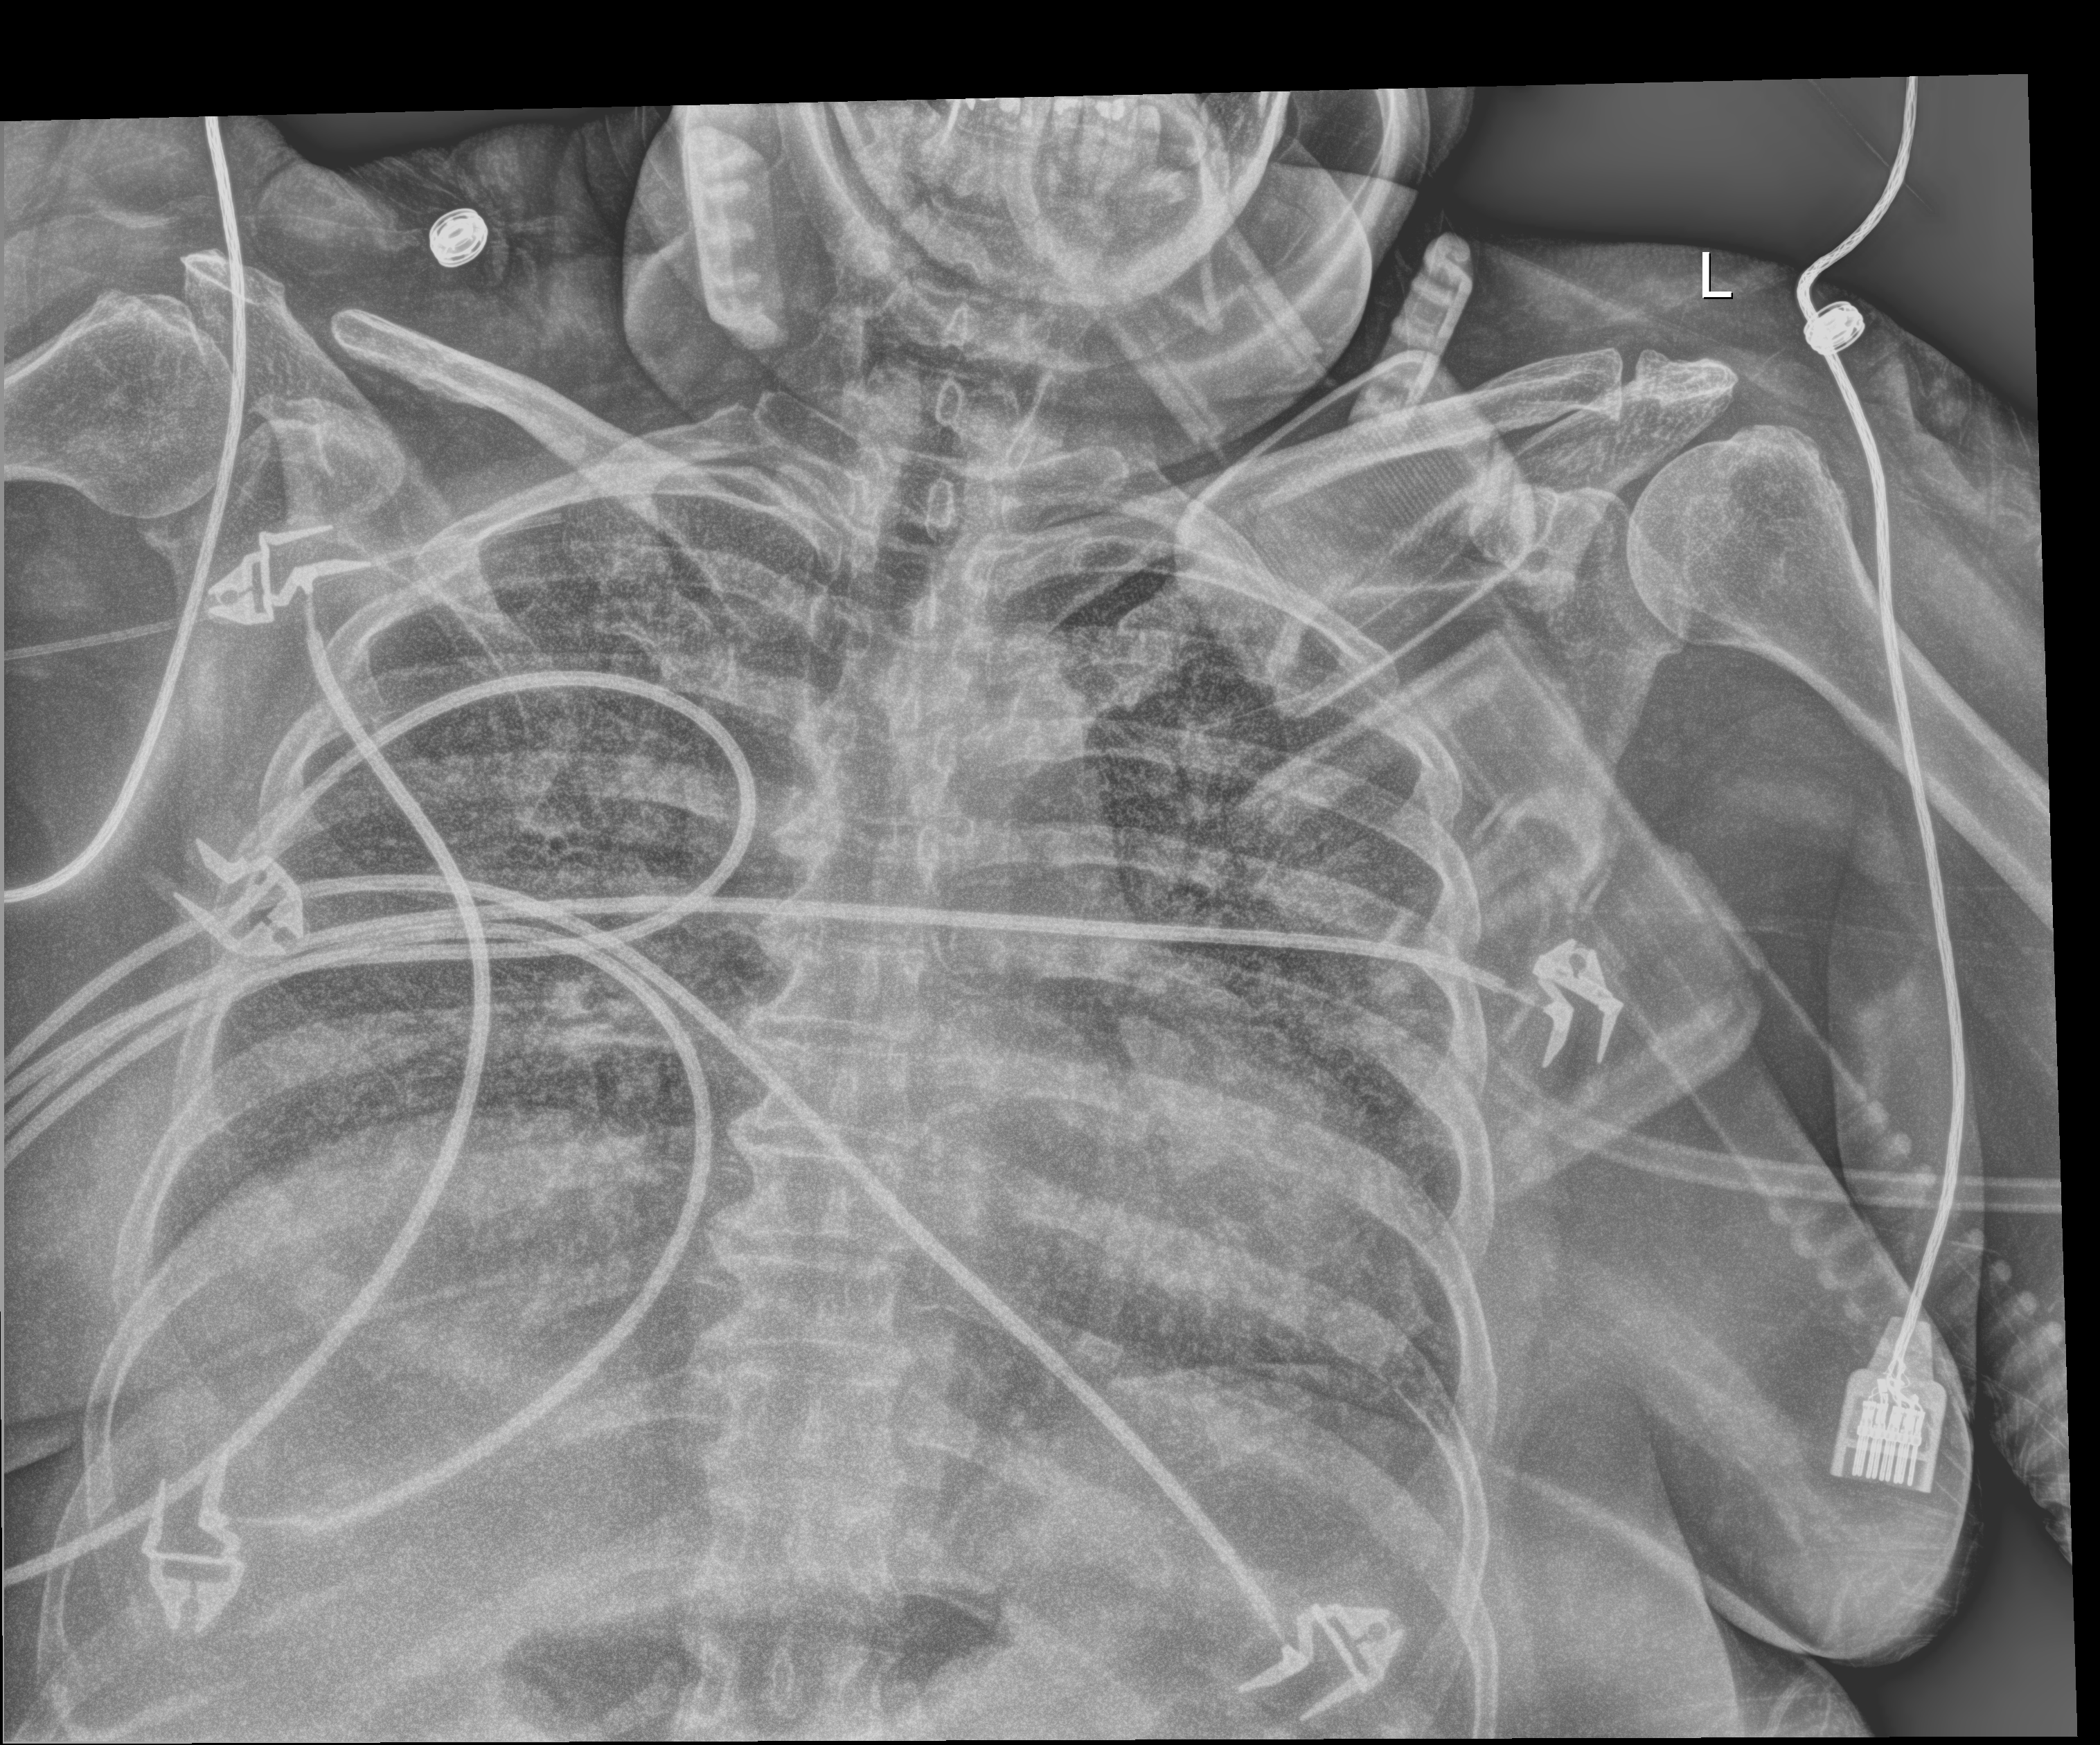
Portable chest radiograph, anteroposterior (AP) projection. Female patient hospitalised with COVID-19, age 60–74 years.
Admission-level facts for this patient (not findings on this image; timing relative to this image not recorded): COPD (admission record): no; length of hospital stay: 38 days; mechanically ventilated during this hospital stay: yes.